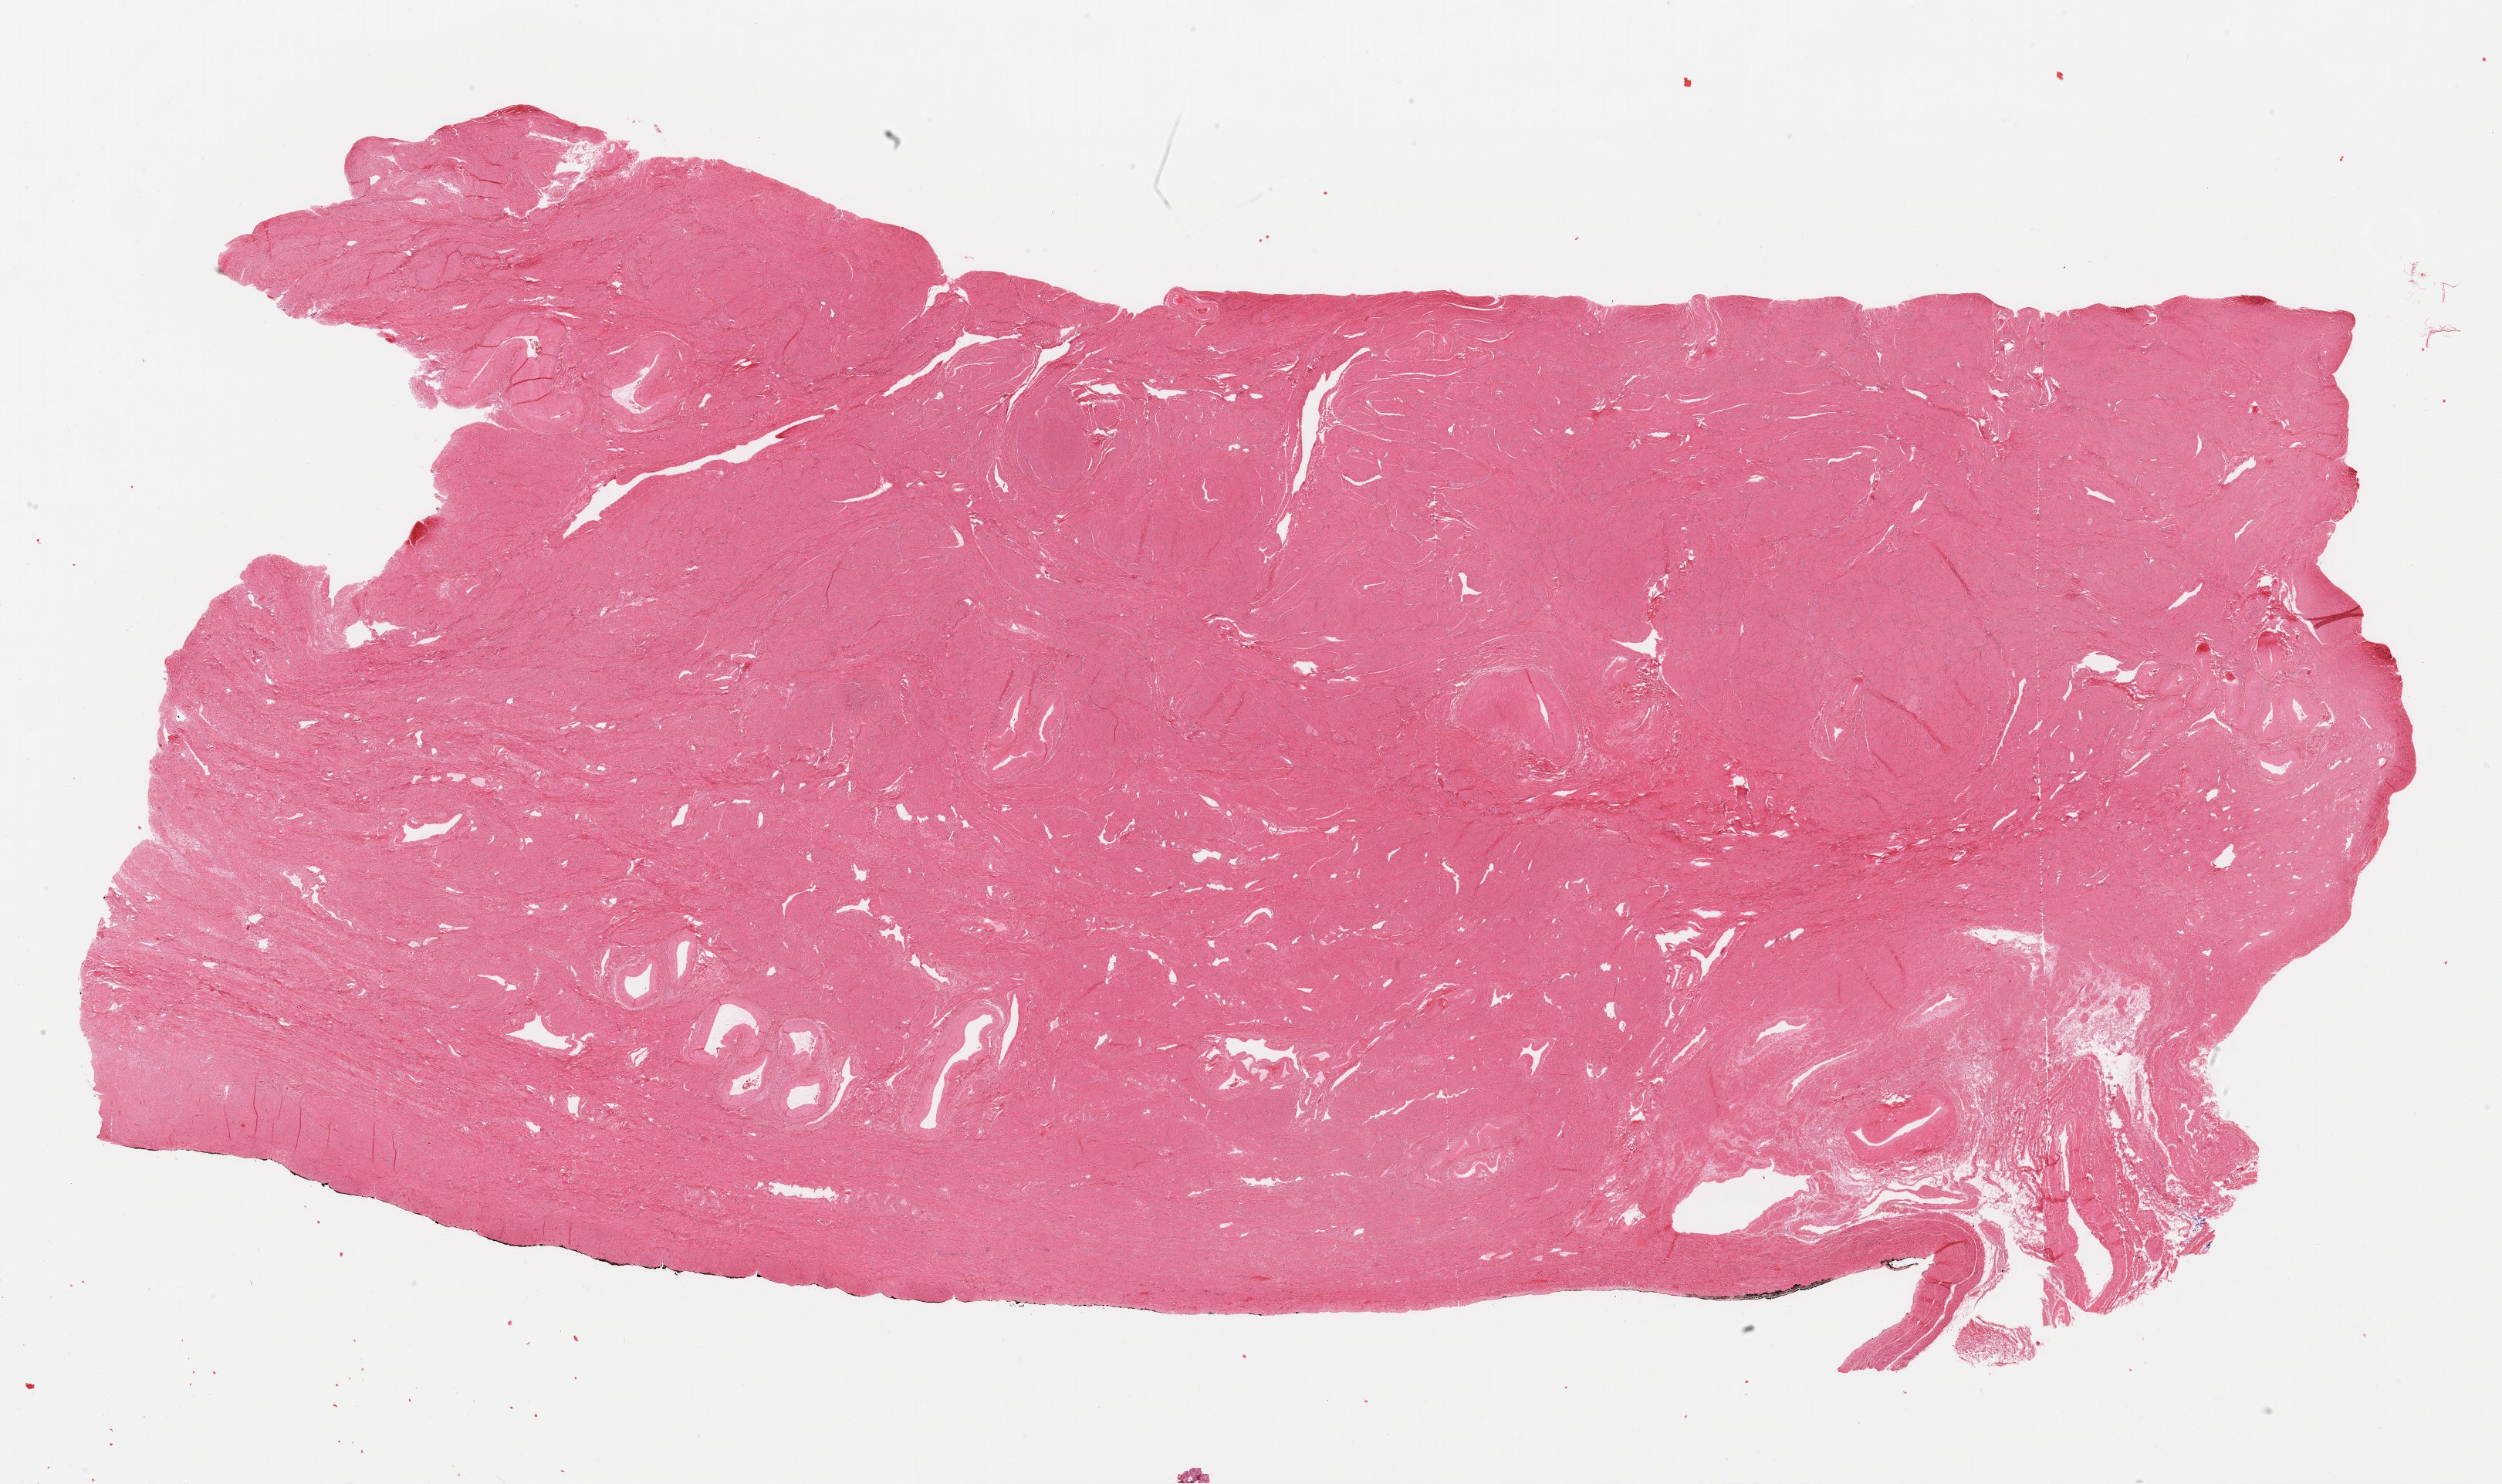
Hematoxylin and eosin (H&E) stained whole-slide image — whole scanned area (about 25.6 x 15.2 mm) shown as a low-resolution overview. Formalin-fixed paraffin-embedded (FFPE) diagnostic section. Uterus, primary tumour sample. Female, age 53 years at initial diagnosis. Histologic grade: G1 (well differentiated).
Pathologic diagnosis: Endometrioid adenocarcinoma, NOS (endometrium). FIGO stage: IB.